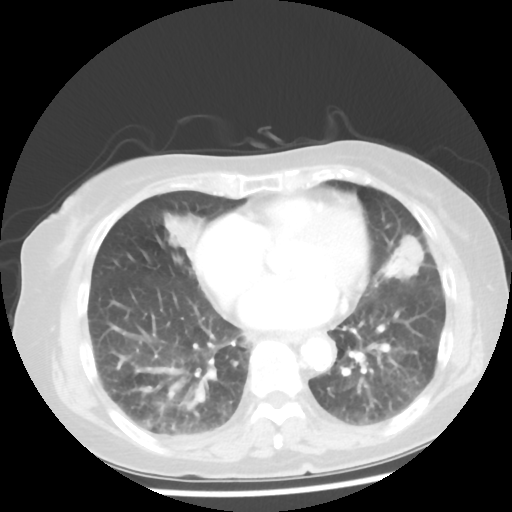
Chest CT, one axial slice; slice 17 of 50 in the series (ordered by position); reconstruction kernel STANDARD; lung window (W 1500 / L -600 HU); 512 × 512 image matrix, field of view 332 × 332 mm. Patient: female, 77 years. From the clinical record (not read from this slice): clinical TNM (as recorded): T2 N3 M1a.
Annotated regions visible in this slice (bounding box drawn by a radiologist):
- lung tumour (recorded histology: adenocarcinoma): bounding box [x1, y1, x2, y2] px = [379, 228, 428, 288]